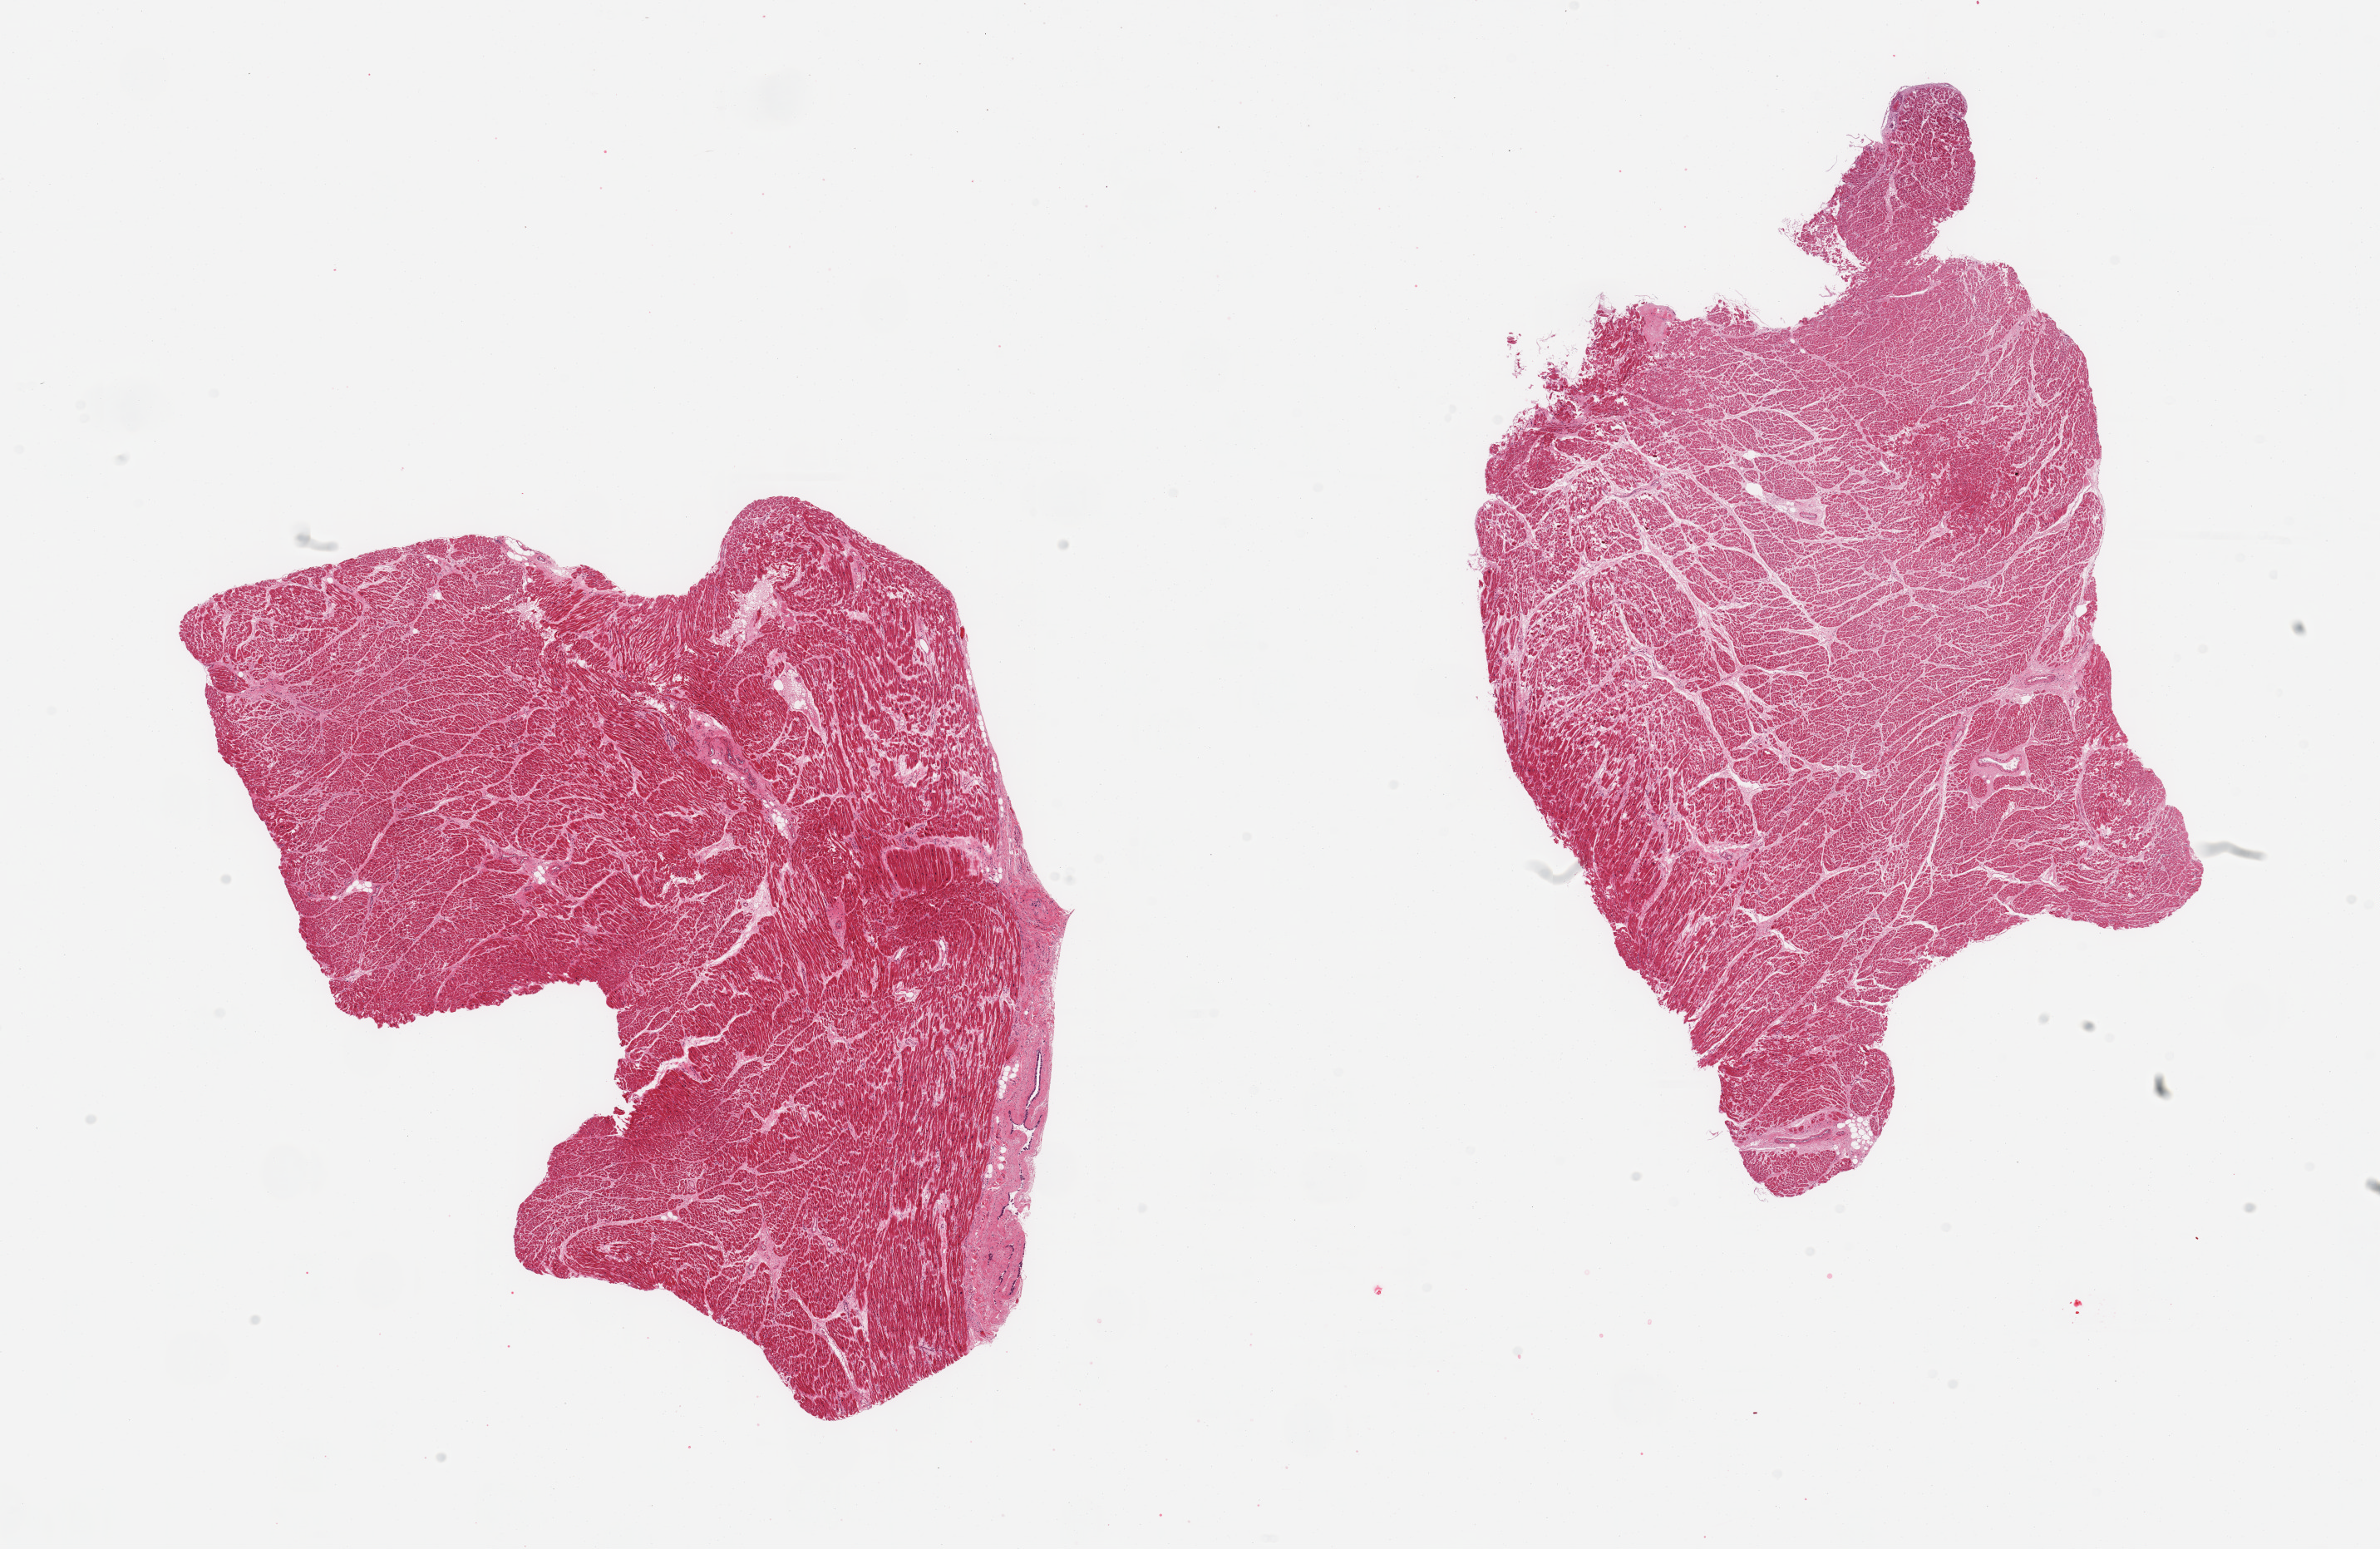
Hematoxylin and eosin (H&E) whole-slide image — a low-resolution overview of the entire scanned area, about 22.6 x 14.7 mm (slide scanned at 20x); PAXgene-fixed paraffin-embedded (PFPE) section; section of heart (target tissue); tissue donor sample. Donor sex: female.
• reviewer comment on this tissue sample: 2 pieces; some increased interstitial fibrosis and hypertrophy